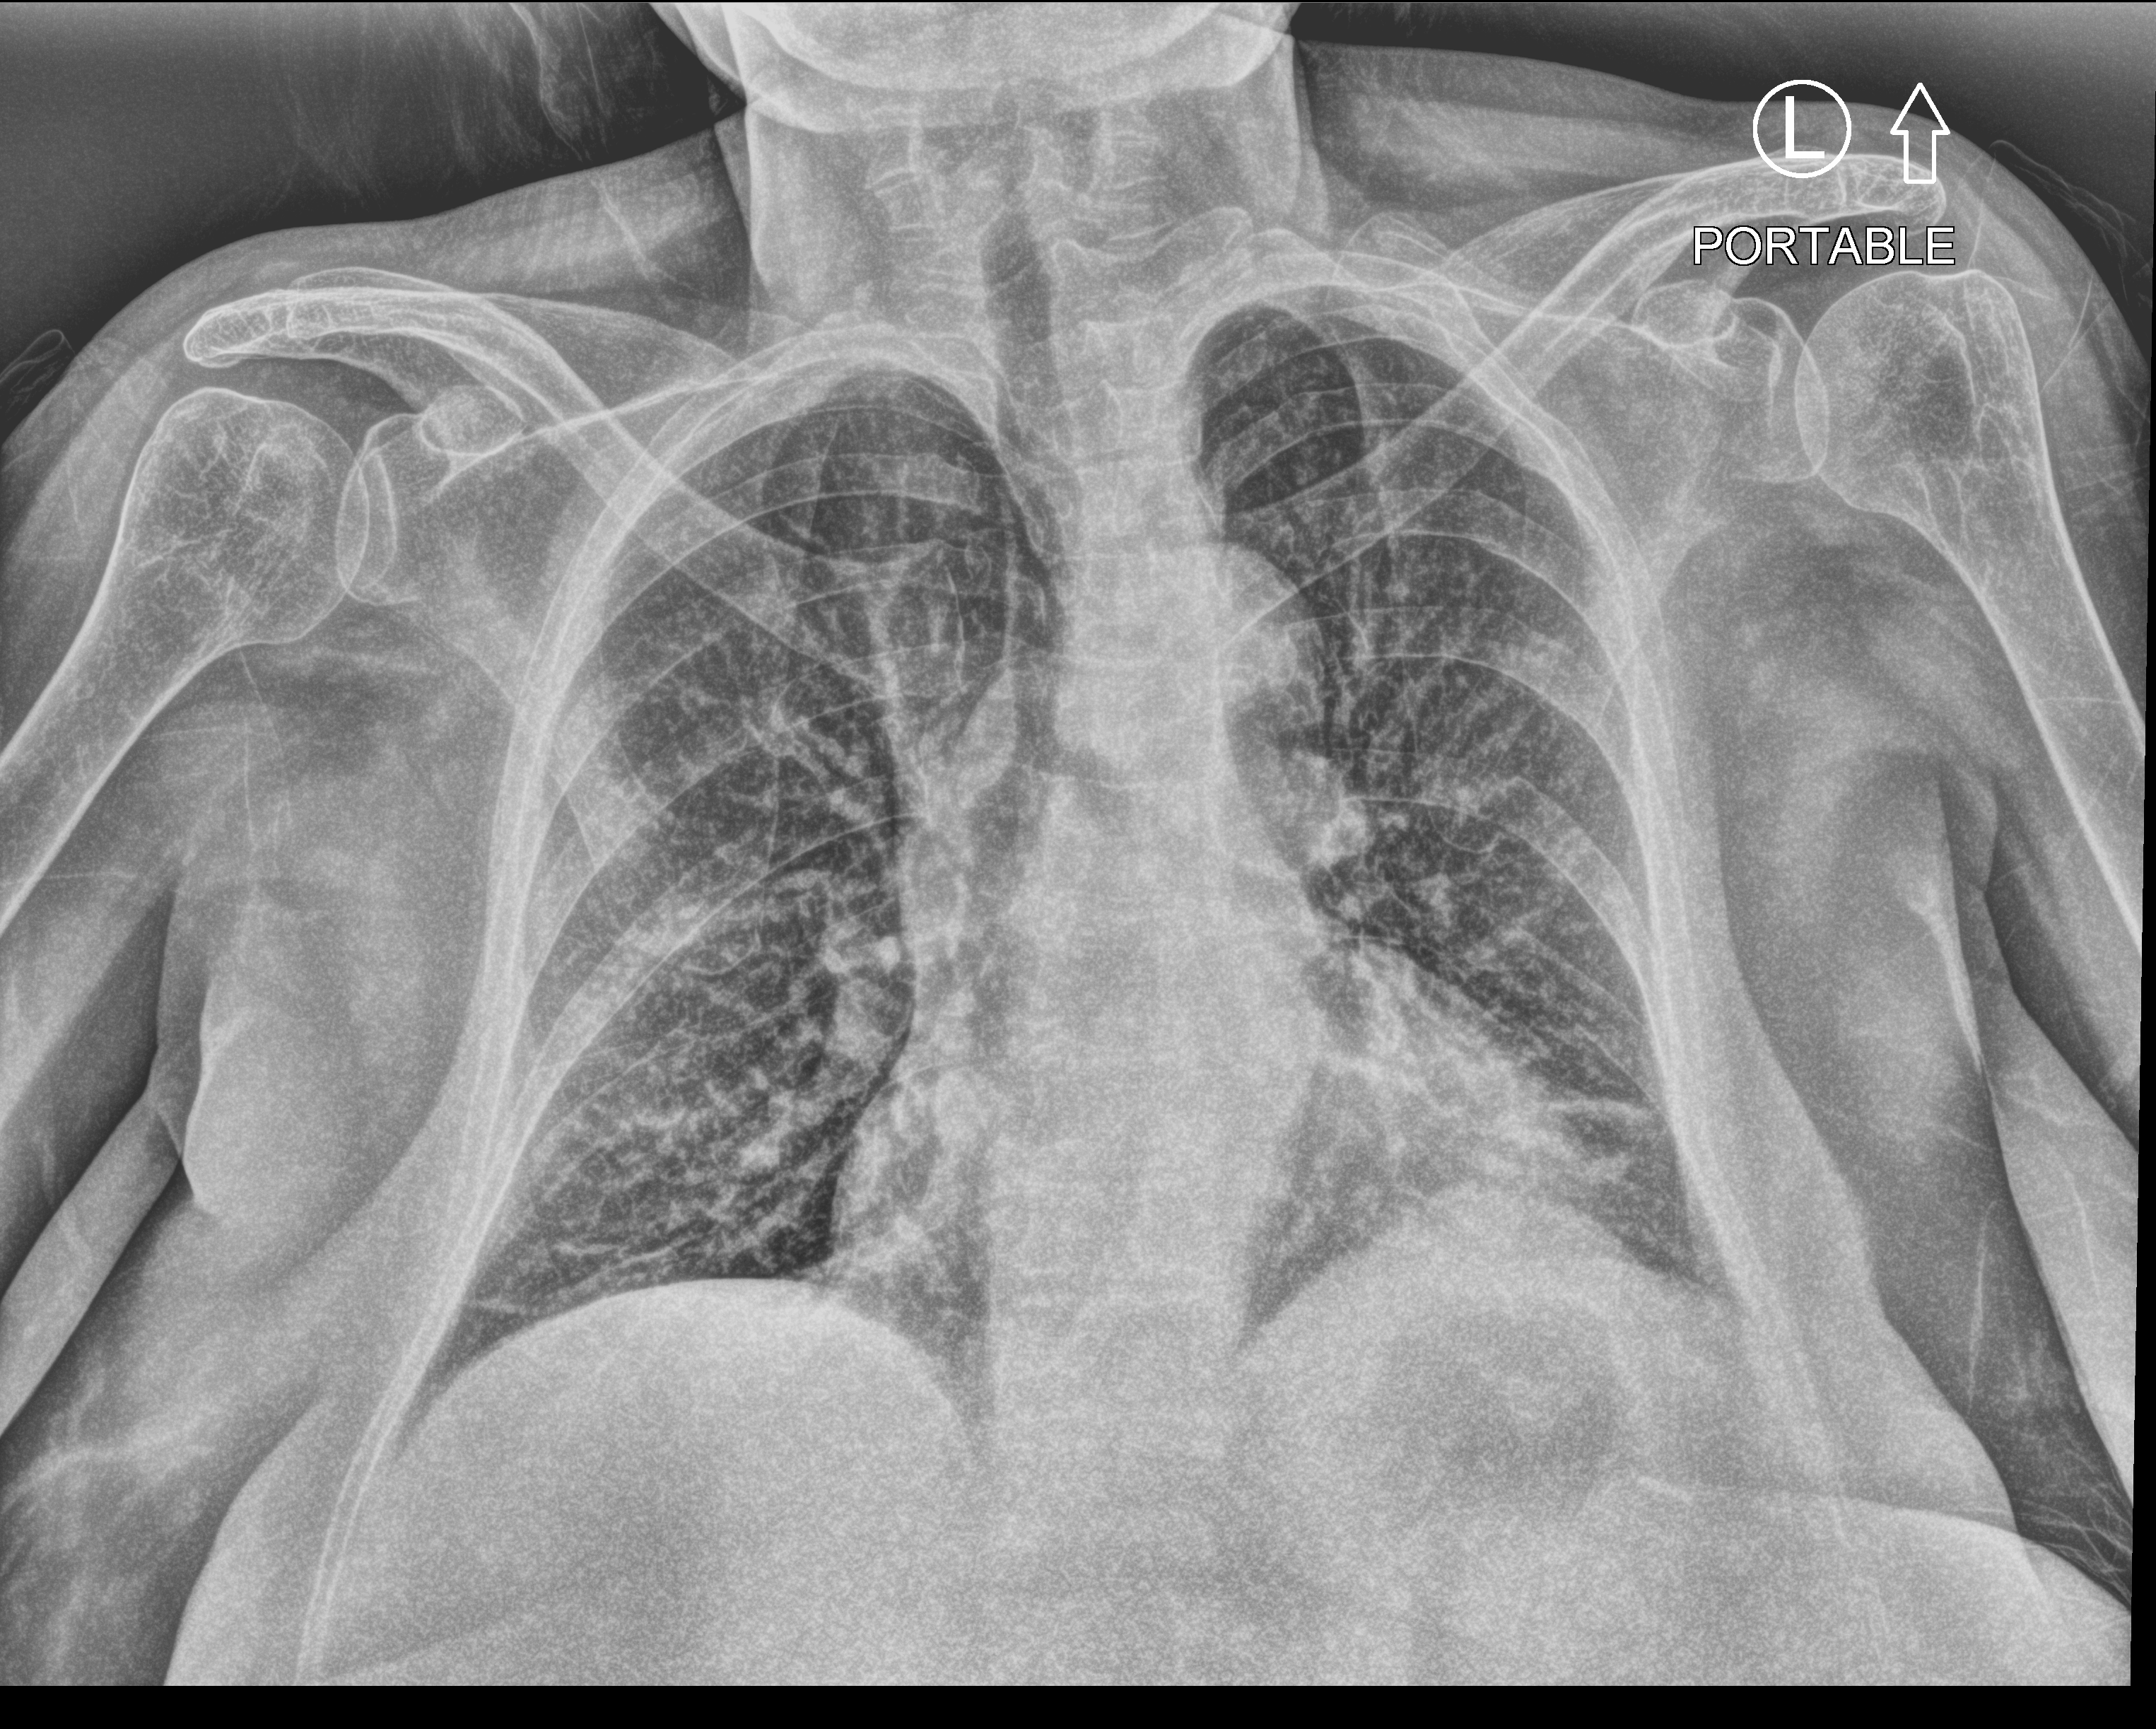
Bedside chest radiograph (computed radiography). Patient hospitalised with COVID-19; female, aged 60–74 years.
Hospital-stay facts (about this admission, not read from this image; timing relative to this image not recorded):
- admitted to intensive care during this hospital stay: no
- length of hospital stay: 1 day